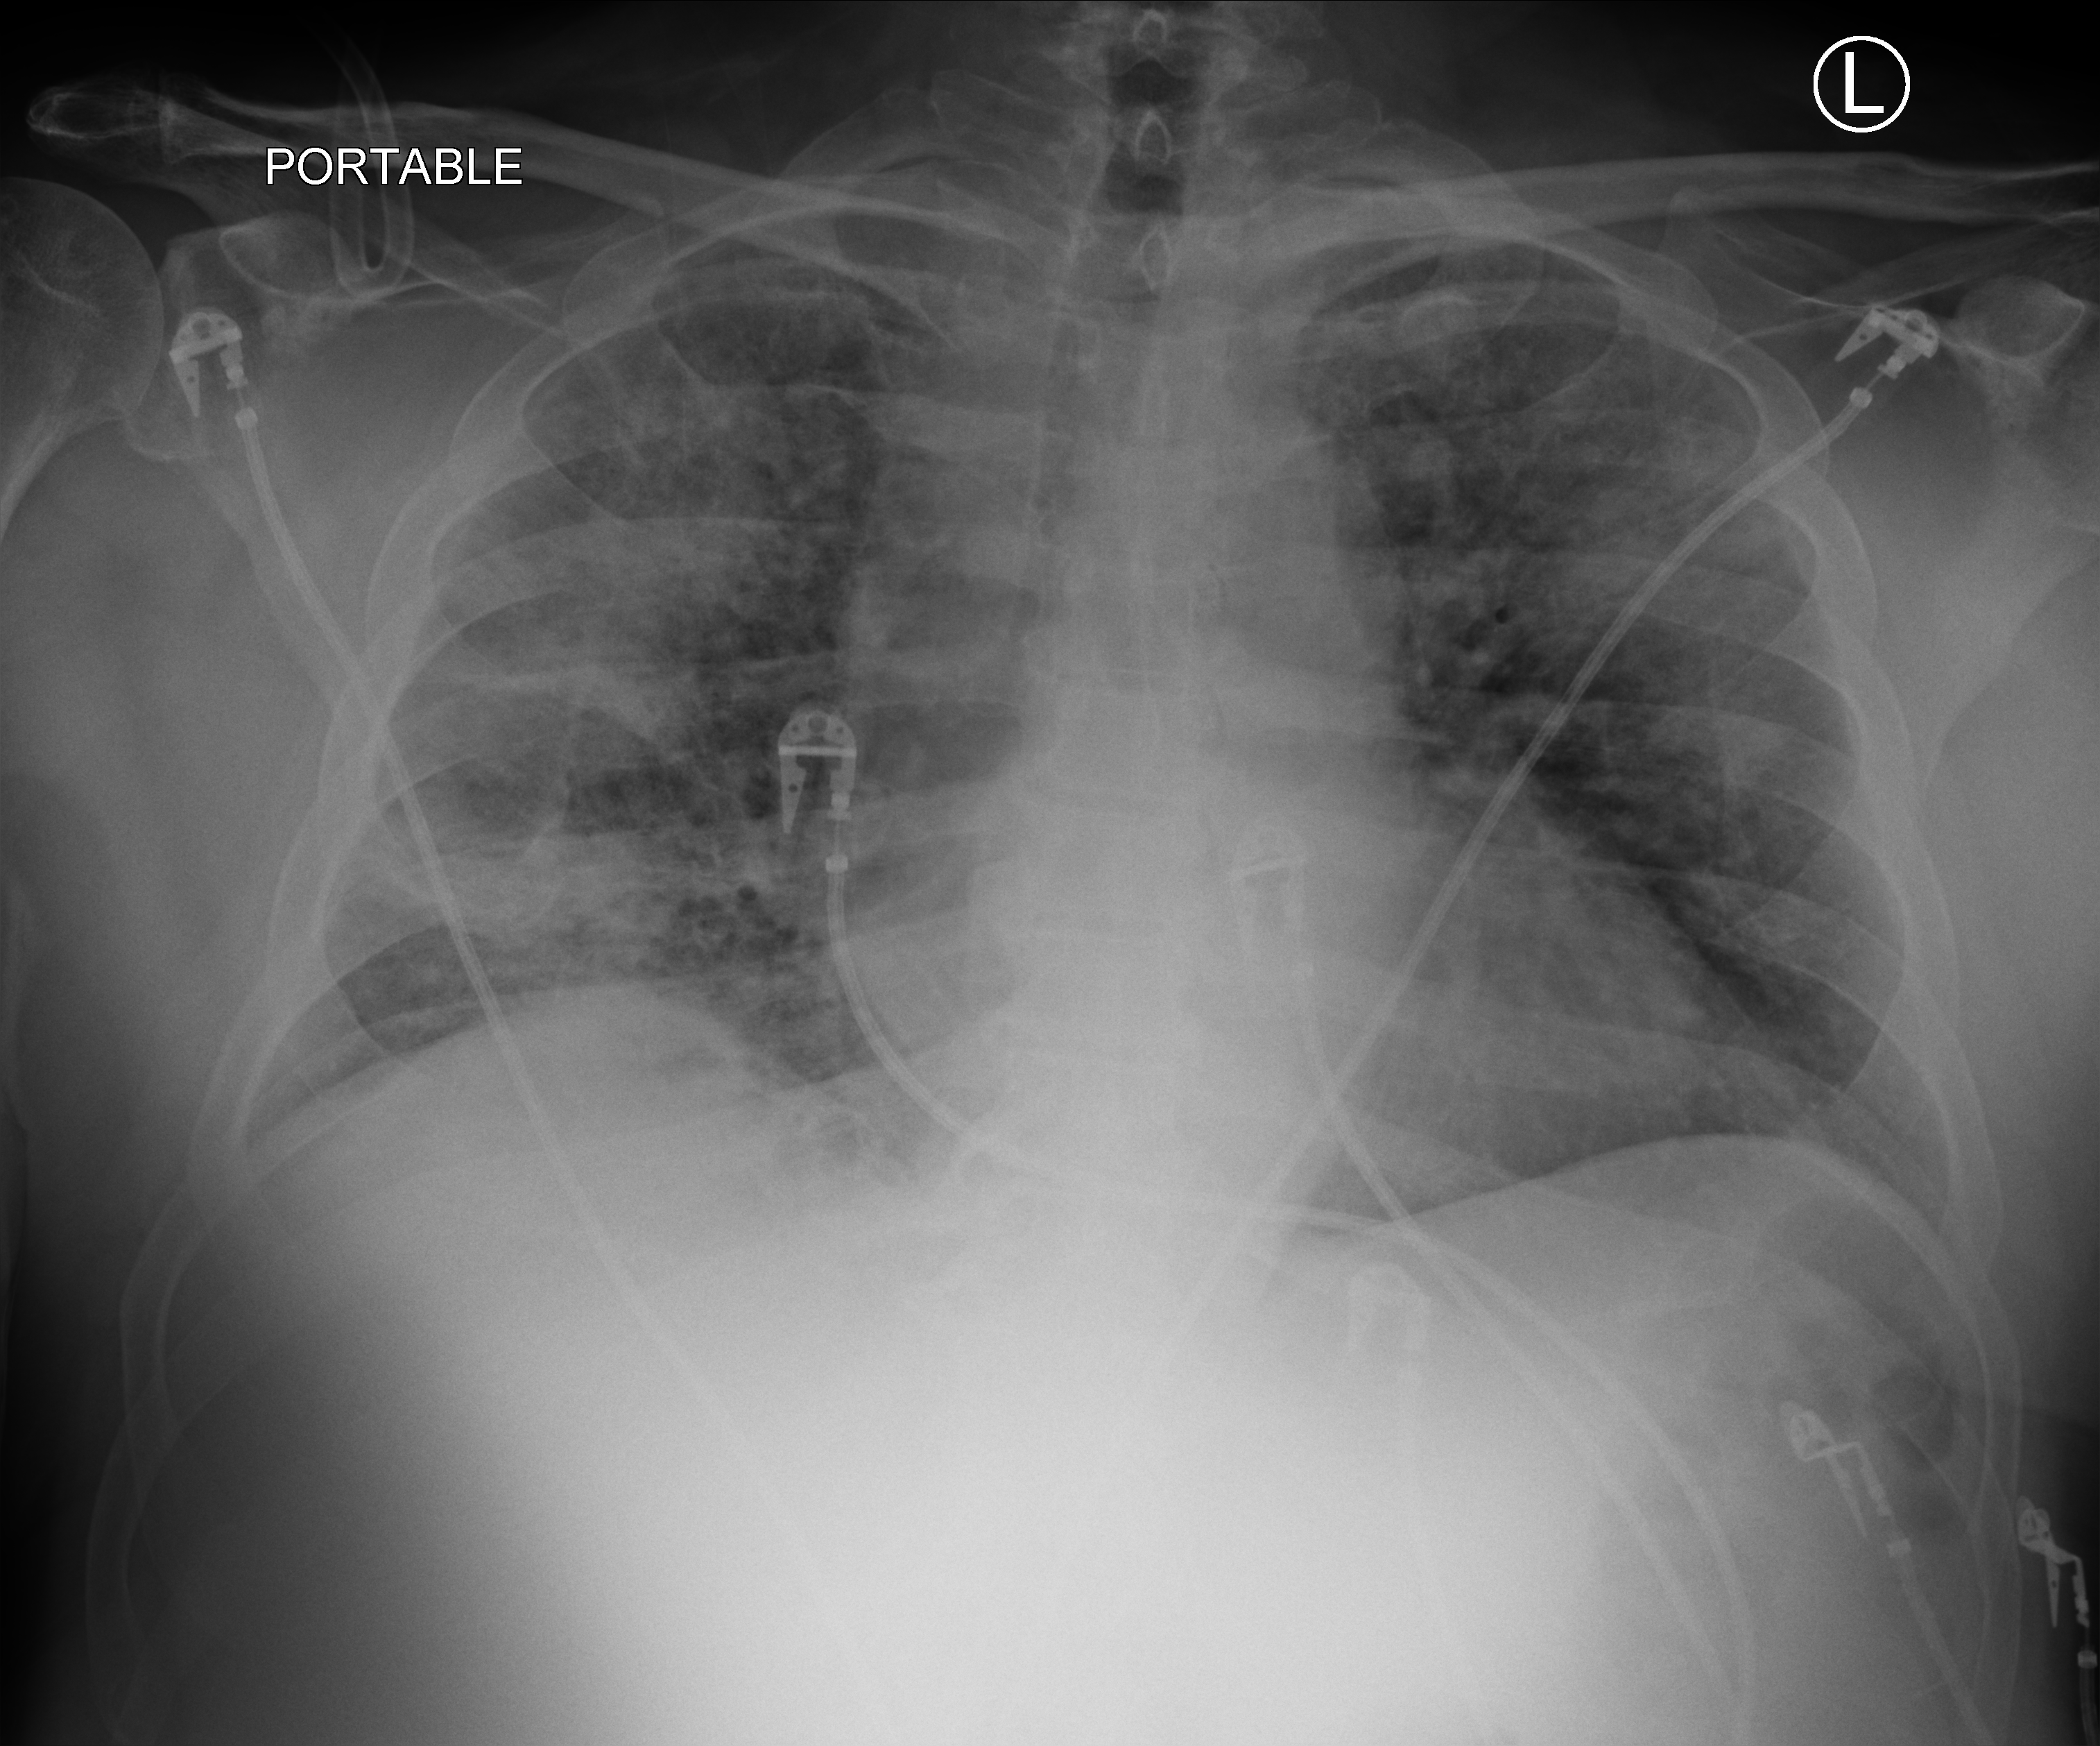
Chest X-ray (portable); anteroposterior (AP) projection. Patient hospitalised with COVID-19; male, aged 60–74 years.
From the hospital-stay record, not from the radiograph (when in the stay this image was taken is not recorded): admitted to intensive care during this hospital stay: yes; mechanically ventilated during this hospital stay: yes; length of hospital stay: 33 days.